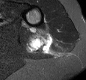
MRI of an extremity soft-tissue mass, one axial slice. Slice 7 of 30 in the series (ordered by position). STIR. MR volume resampled by the dataset authors to the PET/CT grid (not the native acquisition matrix). 3.27 mm slice thickness. 86 × 80 image matrix, field of view 84 × 78 mm. Female patient. From the clinical record (not read from this slice): histological type: malignant fibrous histiocytoma; grade: low; site of the primary tumour: left arm.
Outlined on this slice (expert contour drawn on MRI and transferred to this co-registered scan by the dataset authors):
- gross tumour volume (mass): box from (x=26, y=28) to (x=52, y=55) px